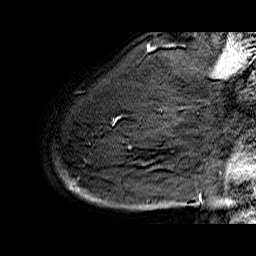
Breast MRI (dynamic contrast-enhanced), one sagittal slice; slice 50 of 60 in the series (ordered by position); dynamic contrast-enhanced series, time point 2 of 6 at this slice position (early post-contrast); 1.5 T; TE 6.4 ms, TR 32.9 ms; 4 mm slice thickness; 256 × 256 image matrix, field of view 200 × 200 mm. Female patient. From the clinical record (not read from this slice): setting: breast cancer imaged before/during neoadjuvant chemotherapy; receptor status: HR-positive, HER2-negative.
Outlined on this slice (semi-automatic segmentation, software-assisted and operator-edited):
- analysis volume of interest (the breast-tissue region the enhancement analysis was run in; not a lesion): box from (x=60, y=74) to (x=176, y=210) px
- tumour enhancement mask (voxels above the 100 % enhancement threshold inside the analysis volume of interest): (x=69, y=184)–(x=79, y=190)